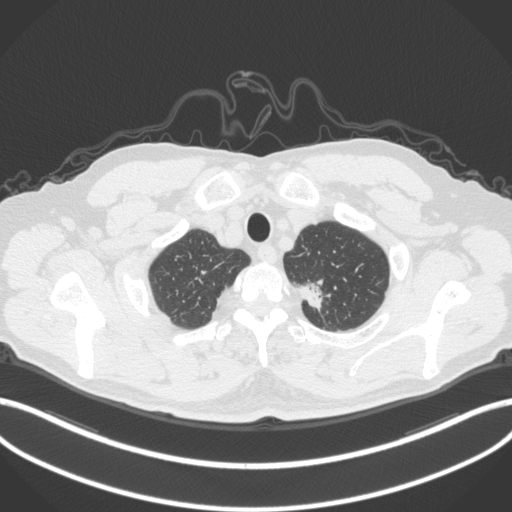
Chest CT, one axial slice. Position 342 of 382 along the scan axis. Reconstruction kernel B31f. 120 kVp. Lung window (W 1500 / L -600 HU). 1 mm slice thickness. 512 × 512 image matrix. Male patient, age 64 years. Case-level facts recorded for this patient, not image findings: clinical TNM (as recorded): T1c N0 M0.
Structures marked on this image (rectangle marked by the reading radiologist):
- lung tumour (recorded histology: adenocarcinoma): bounding box <294,277,330,316> (left, top, right, bottom; pixels)